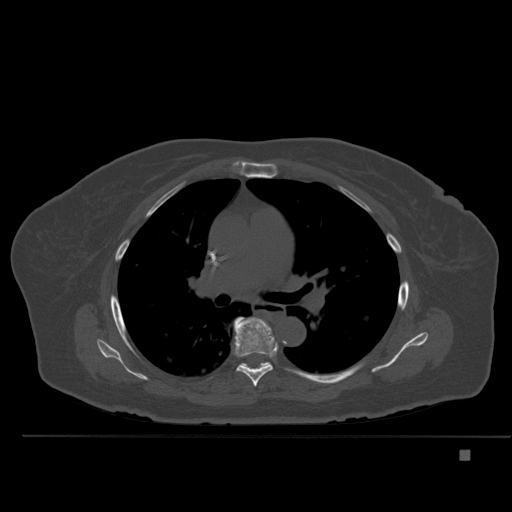
CT including the spine, one axial slice; slice 337 of 477 in the series (ordered by position); bone window (W 1800 / L 400 HU); 512 × 512 image matrix, field of view 422 × 422 mm. Patient: female, 74 years. From the clinical record (not read from this slice): primary cancer: colon.
Outlined on this slice (semi-automatic segmentation, software-assisted and operator-edited):
- T6 vertebra: box from (x=234, y=317) to (x=275, y=387) px
- T7 vertebra: (x=237, y=317)–(x=269, y=369)